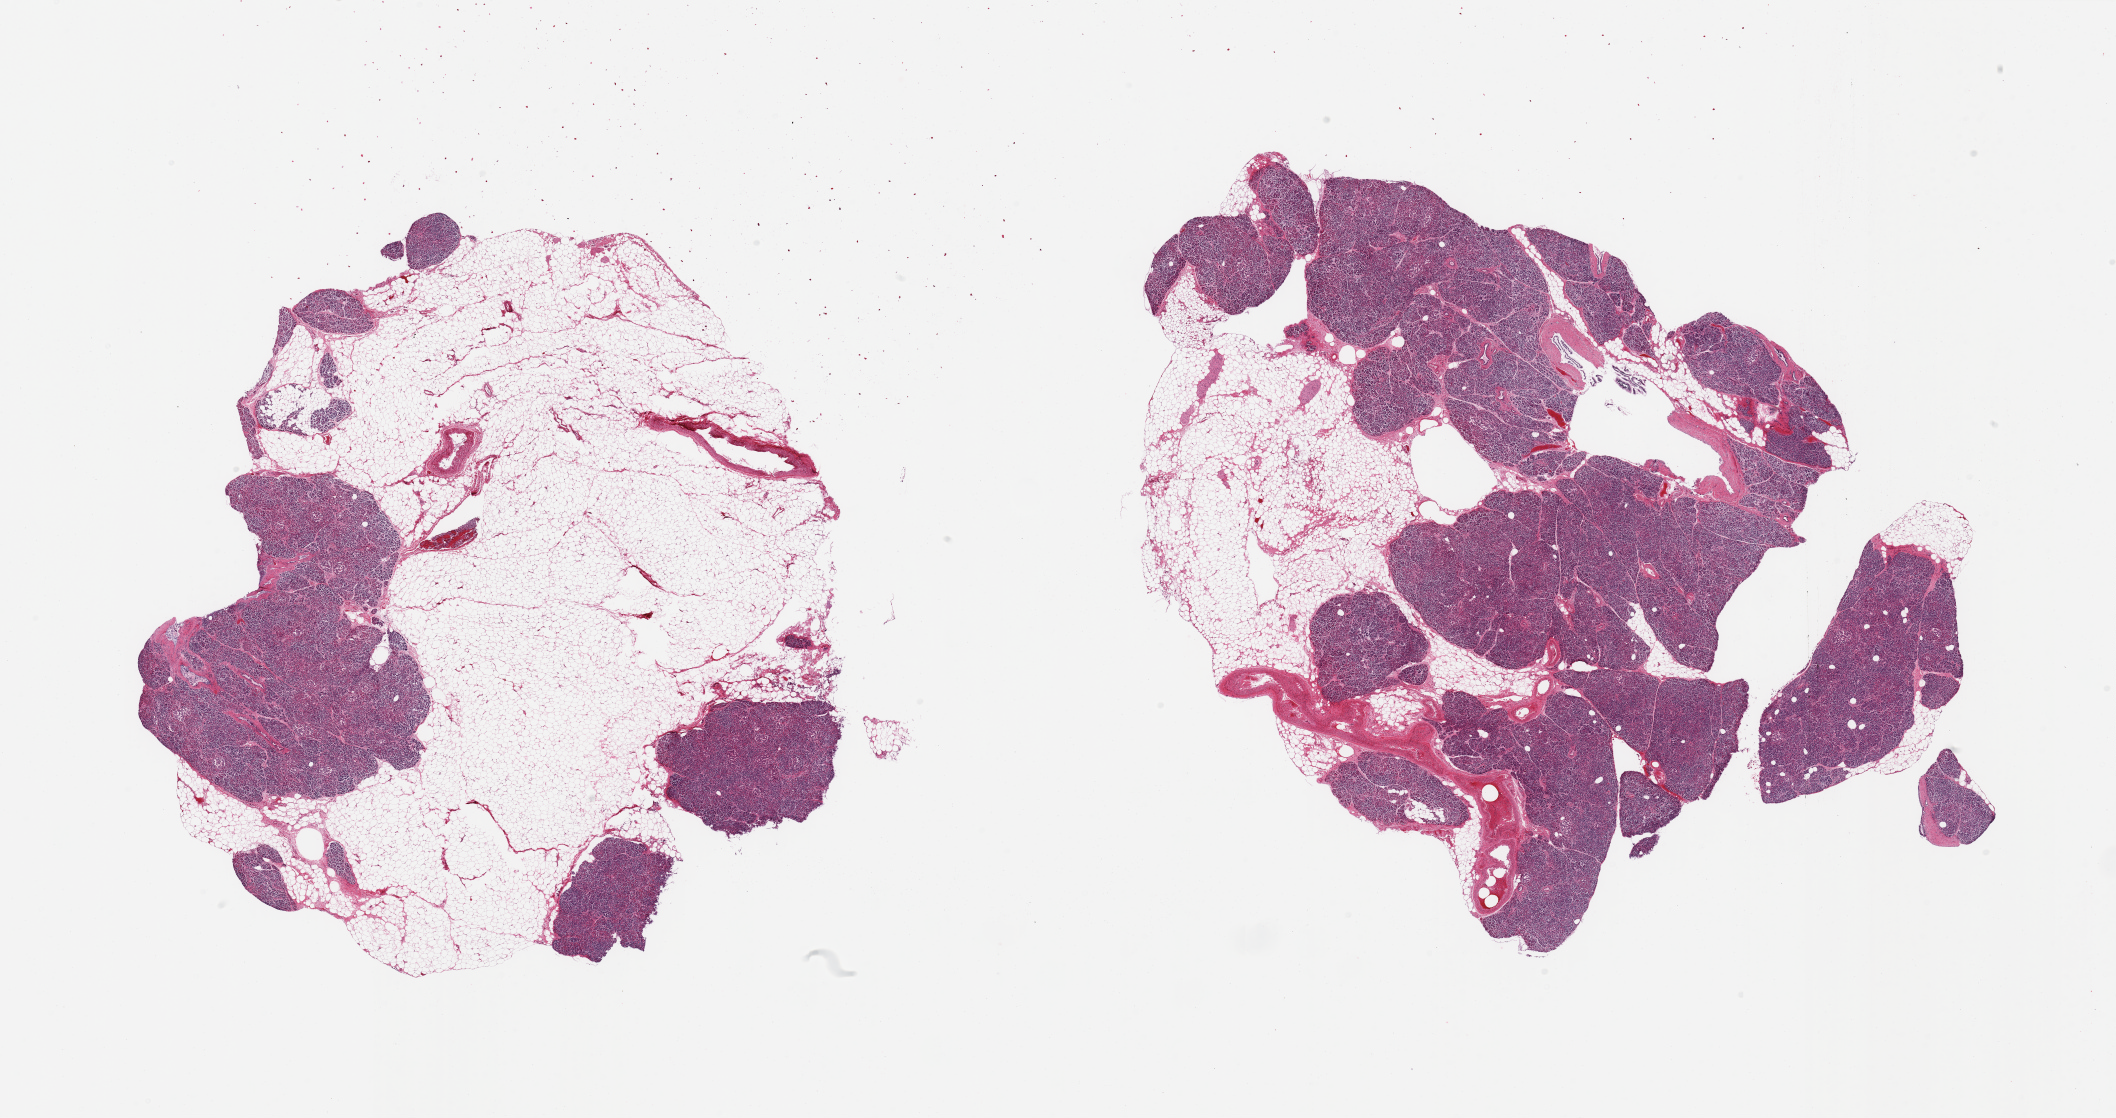
H&E whole-slide image — a low-resolution overview of the entire scanned area, about 33.5 x 17.7 mm; PAXgene-fixed paraffin-embedded (PFPE) section; sampled site (target tissue): pancreas; tissue donor sample. Donor sex: female.
• pathologist's review note for this sample: 2 pieces, ~40% adherent/interstitial fat, rep delinated. Islets poorly preserved, moderately-advanced saponification